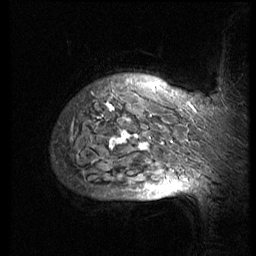
Breast MRI (dynamic contrast-enhanced), one sagittal slice; position 63 of 74 along the scan axis; 3 images stored at this slice position (order not interpretable as contrast timing); 1.5 T; TE 4.2 ms, TR 8.9 ms; 2.5 mm slice thickness; 256 × 256 image matrix. Patient: female, 57 years. Case-level facts recorded for this patient, not image findings: setting: breast cancer imaged before/during neoadjuvant chemotherapy; receptor status: HER2-positive.
Annotated regions visible in this slice (semi-automatically segmented with operator editing):
- analysis volume of interest (the breast-tissue region the enhancement analysis was run in; not a lesion): bounding box <52,68,248,173> (left, top, right, bottom; pixels)
- tumour enhancement mask (voxels above the 140 % enhancement threshold inside the analysis volume of interest): <100,85,195,151>